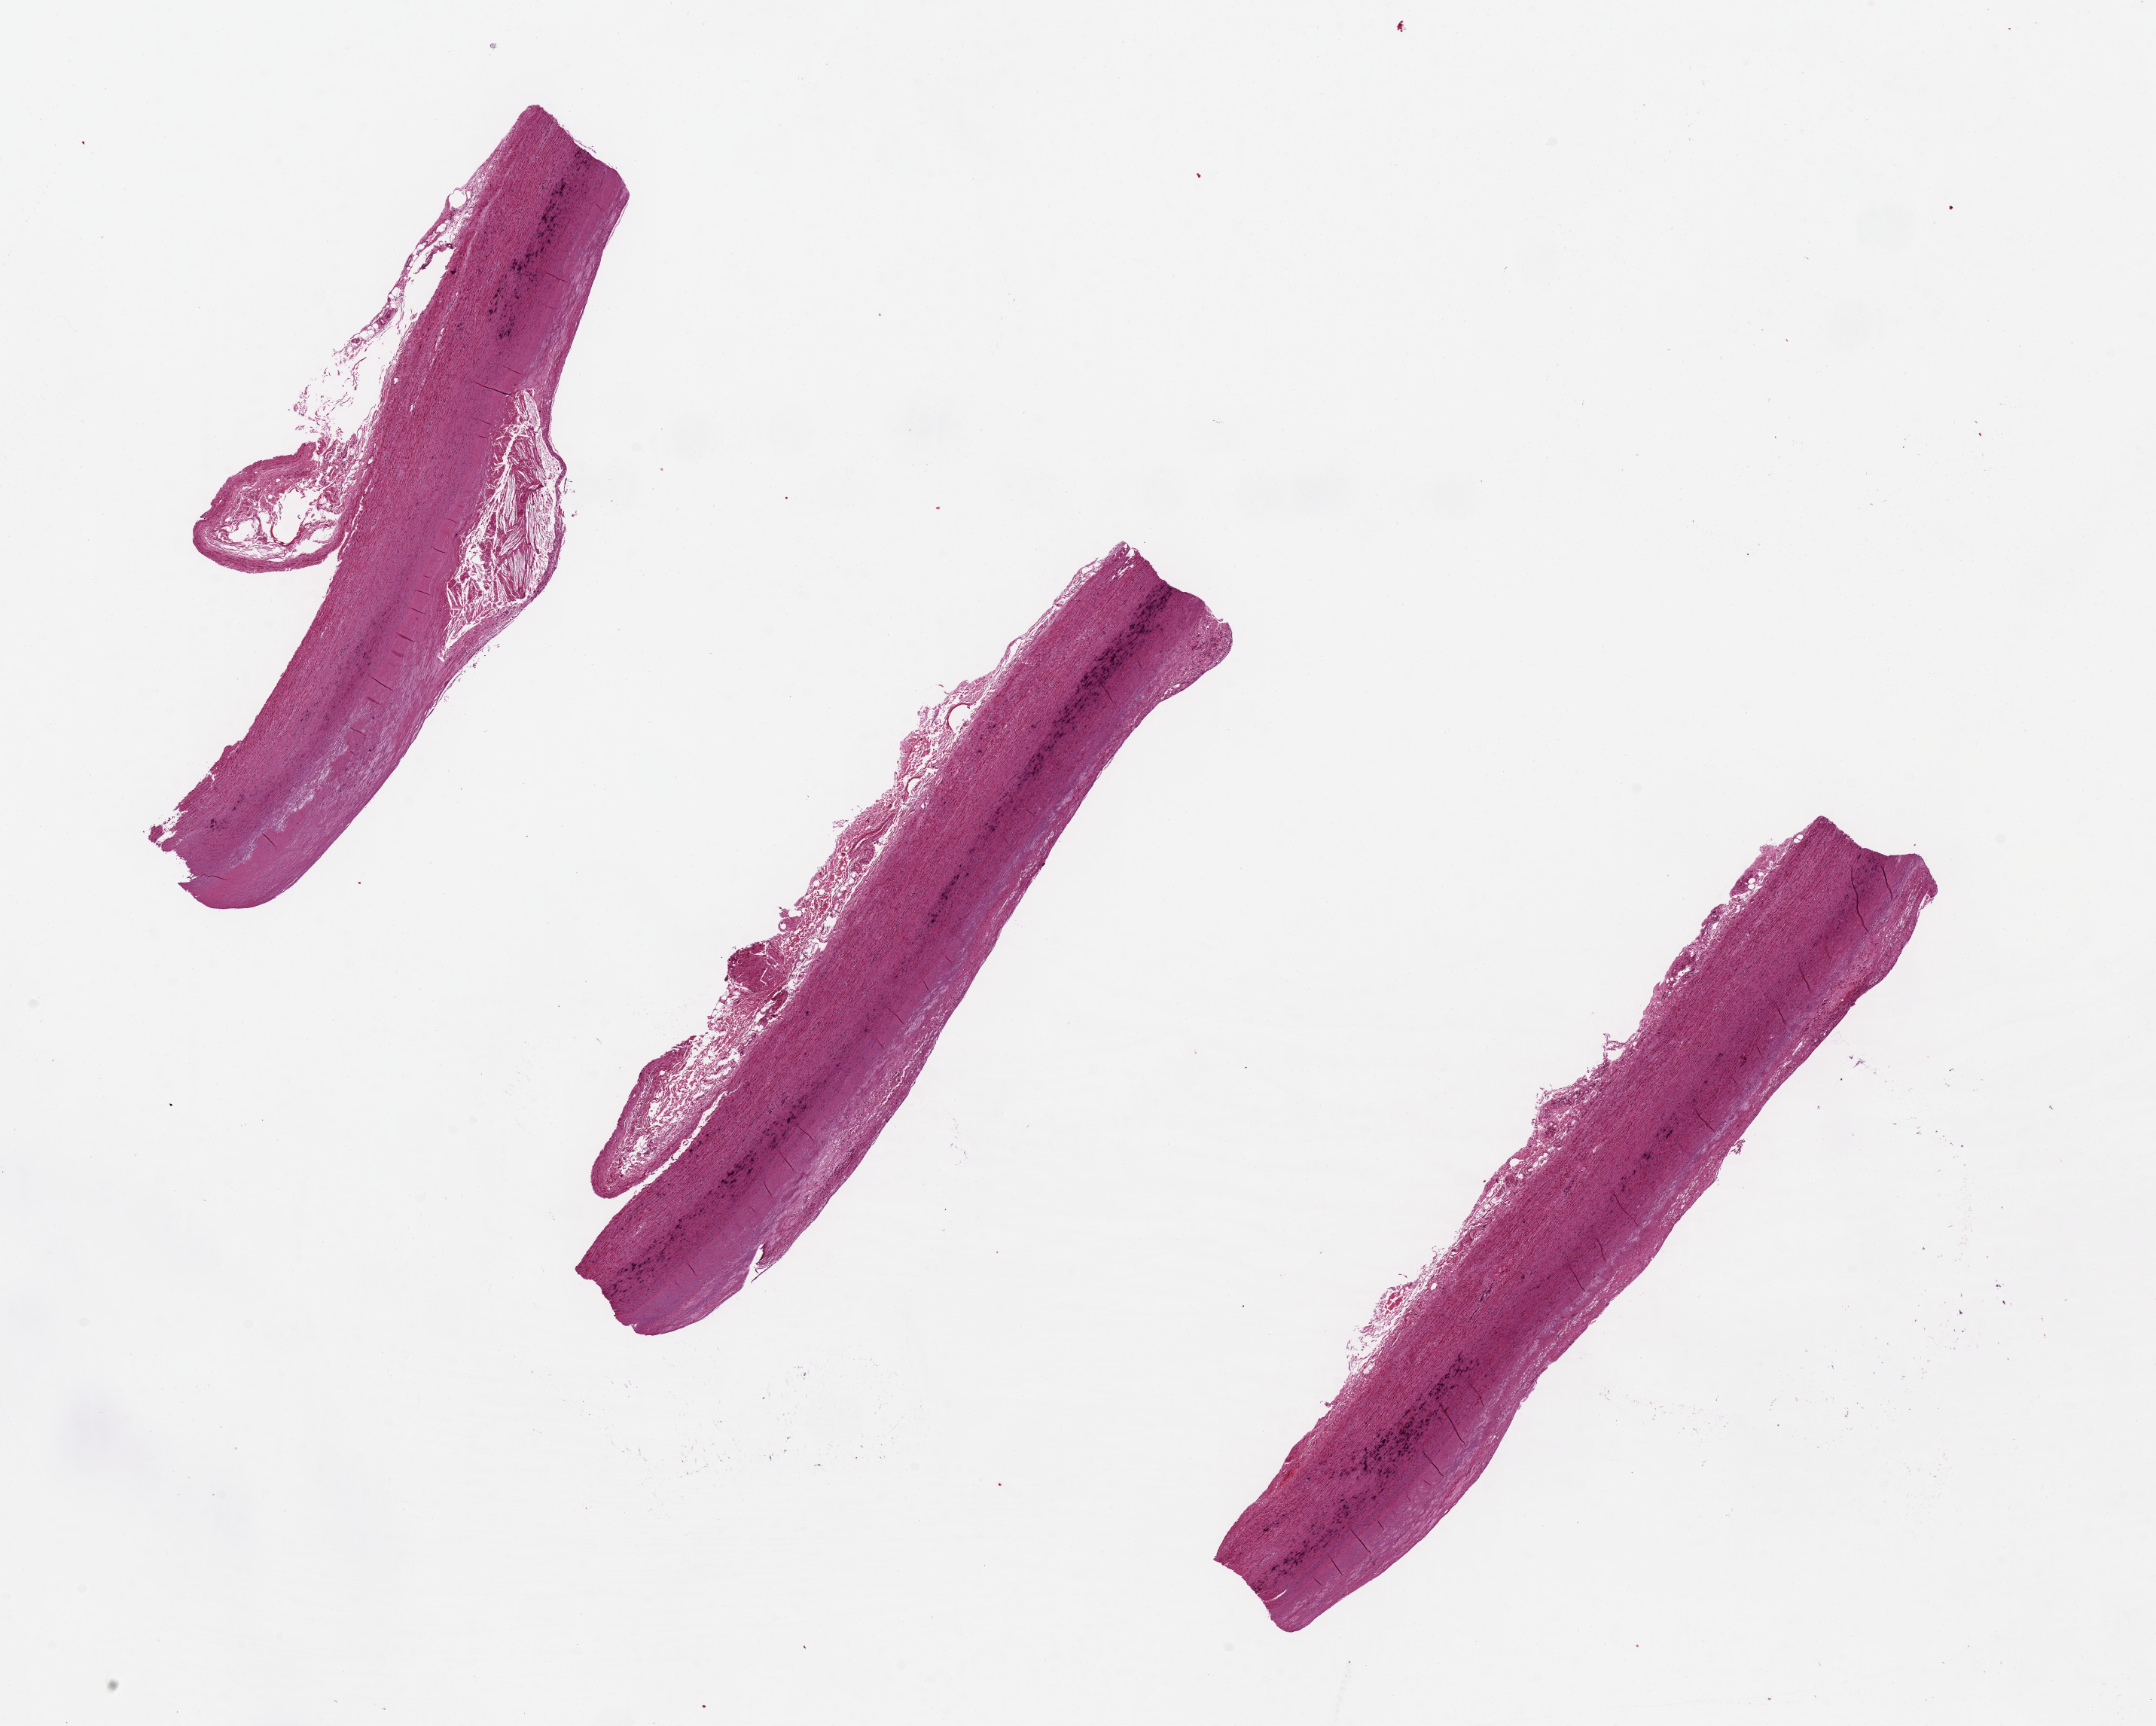
Digitized haematoxylin and eosin-stained section — shown as a low-resolution overview of the whole scanned area (about 22.6 x 18.1 mm); PAXgene-fixed, paraffin-embedded tissue; section of aorta (target tissue); donor tissue sample. Donor sex: male.
Reviewer comment on this tissue sample: Atheromatous plaques. Medial calcification. 10x1.8mm.